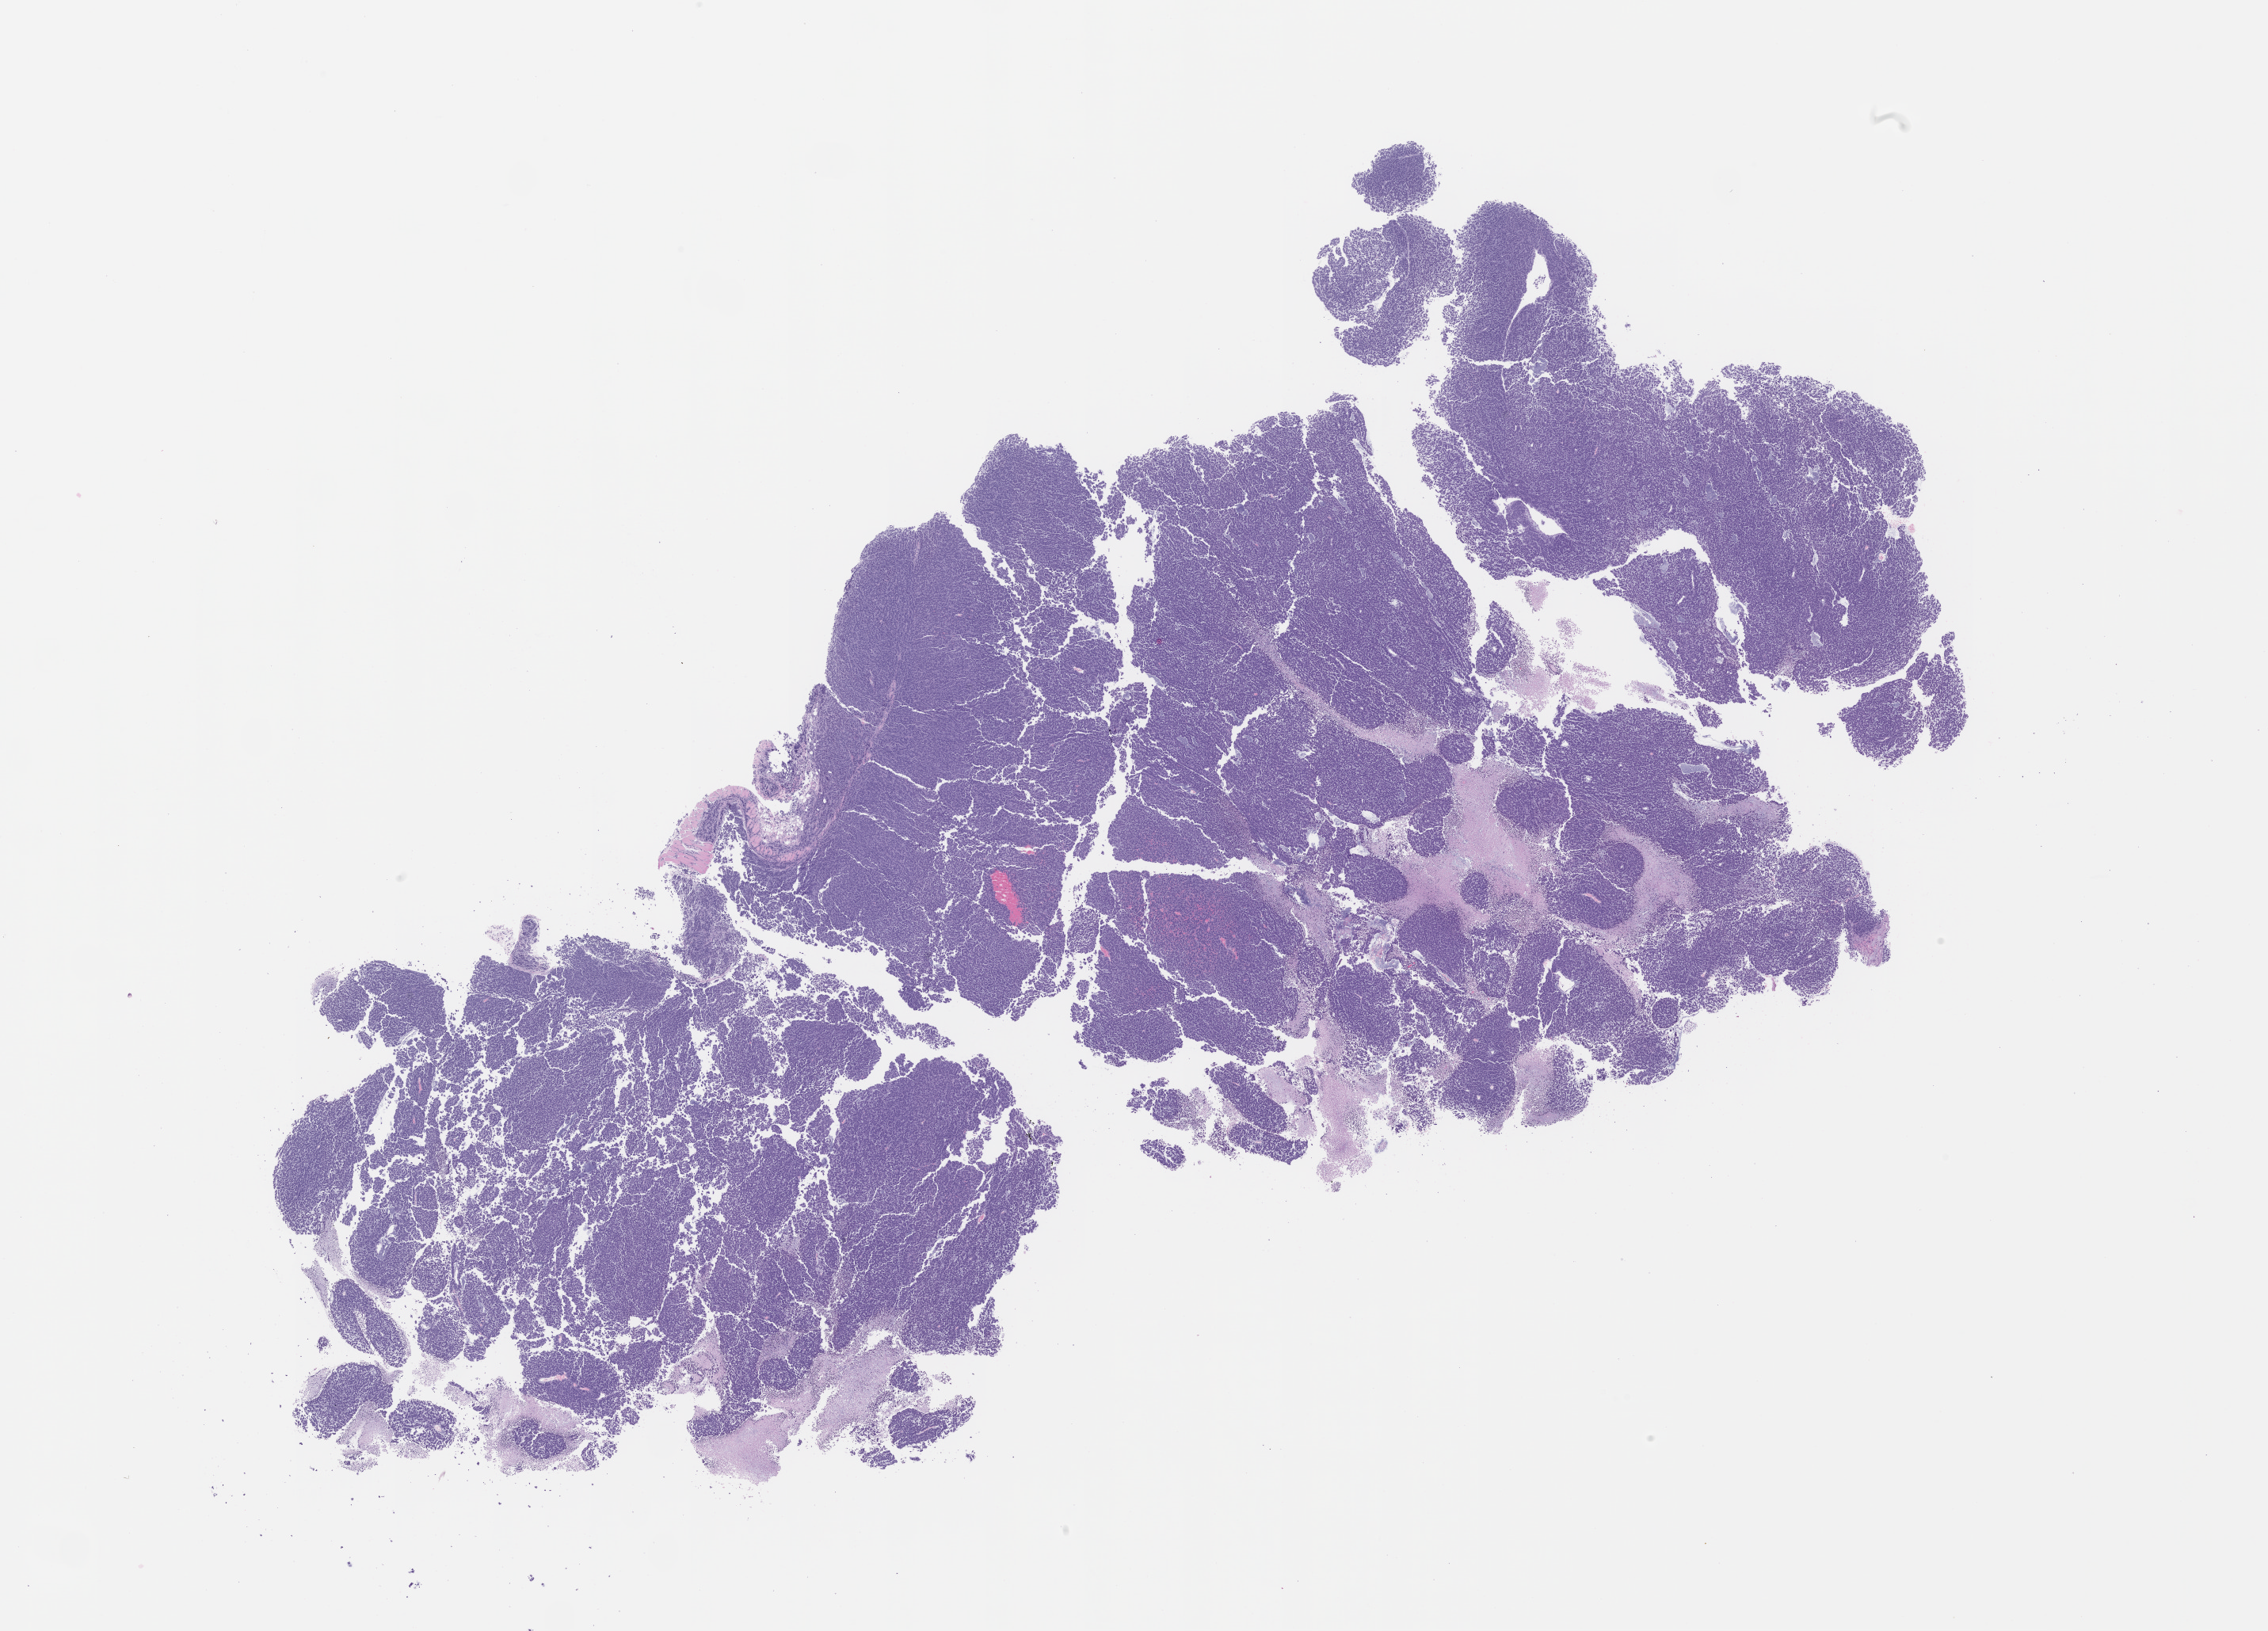
Hematoxylin and eosin (H&E) whole-slide image of a patient-derived xenograft (PDX) tumor grown in a mouse, passage 0 — shown as a low-resolution overview of the whole scanned area (about 22.9 x 16.5 mm), formalin-fixed, paraffin-embedded (FFPE) tissue, originating tumor site category: ovary.
* originating patient diagnosis: Ovarian Carcinoma